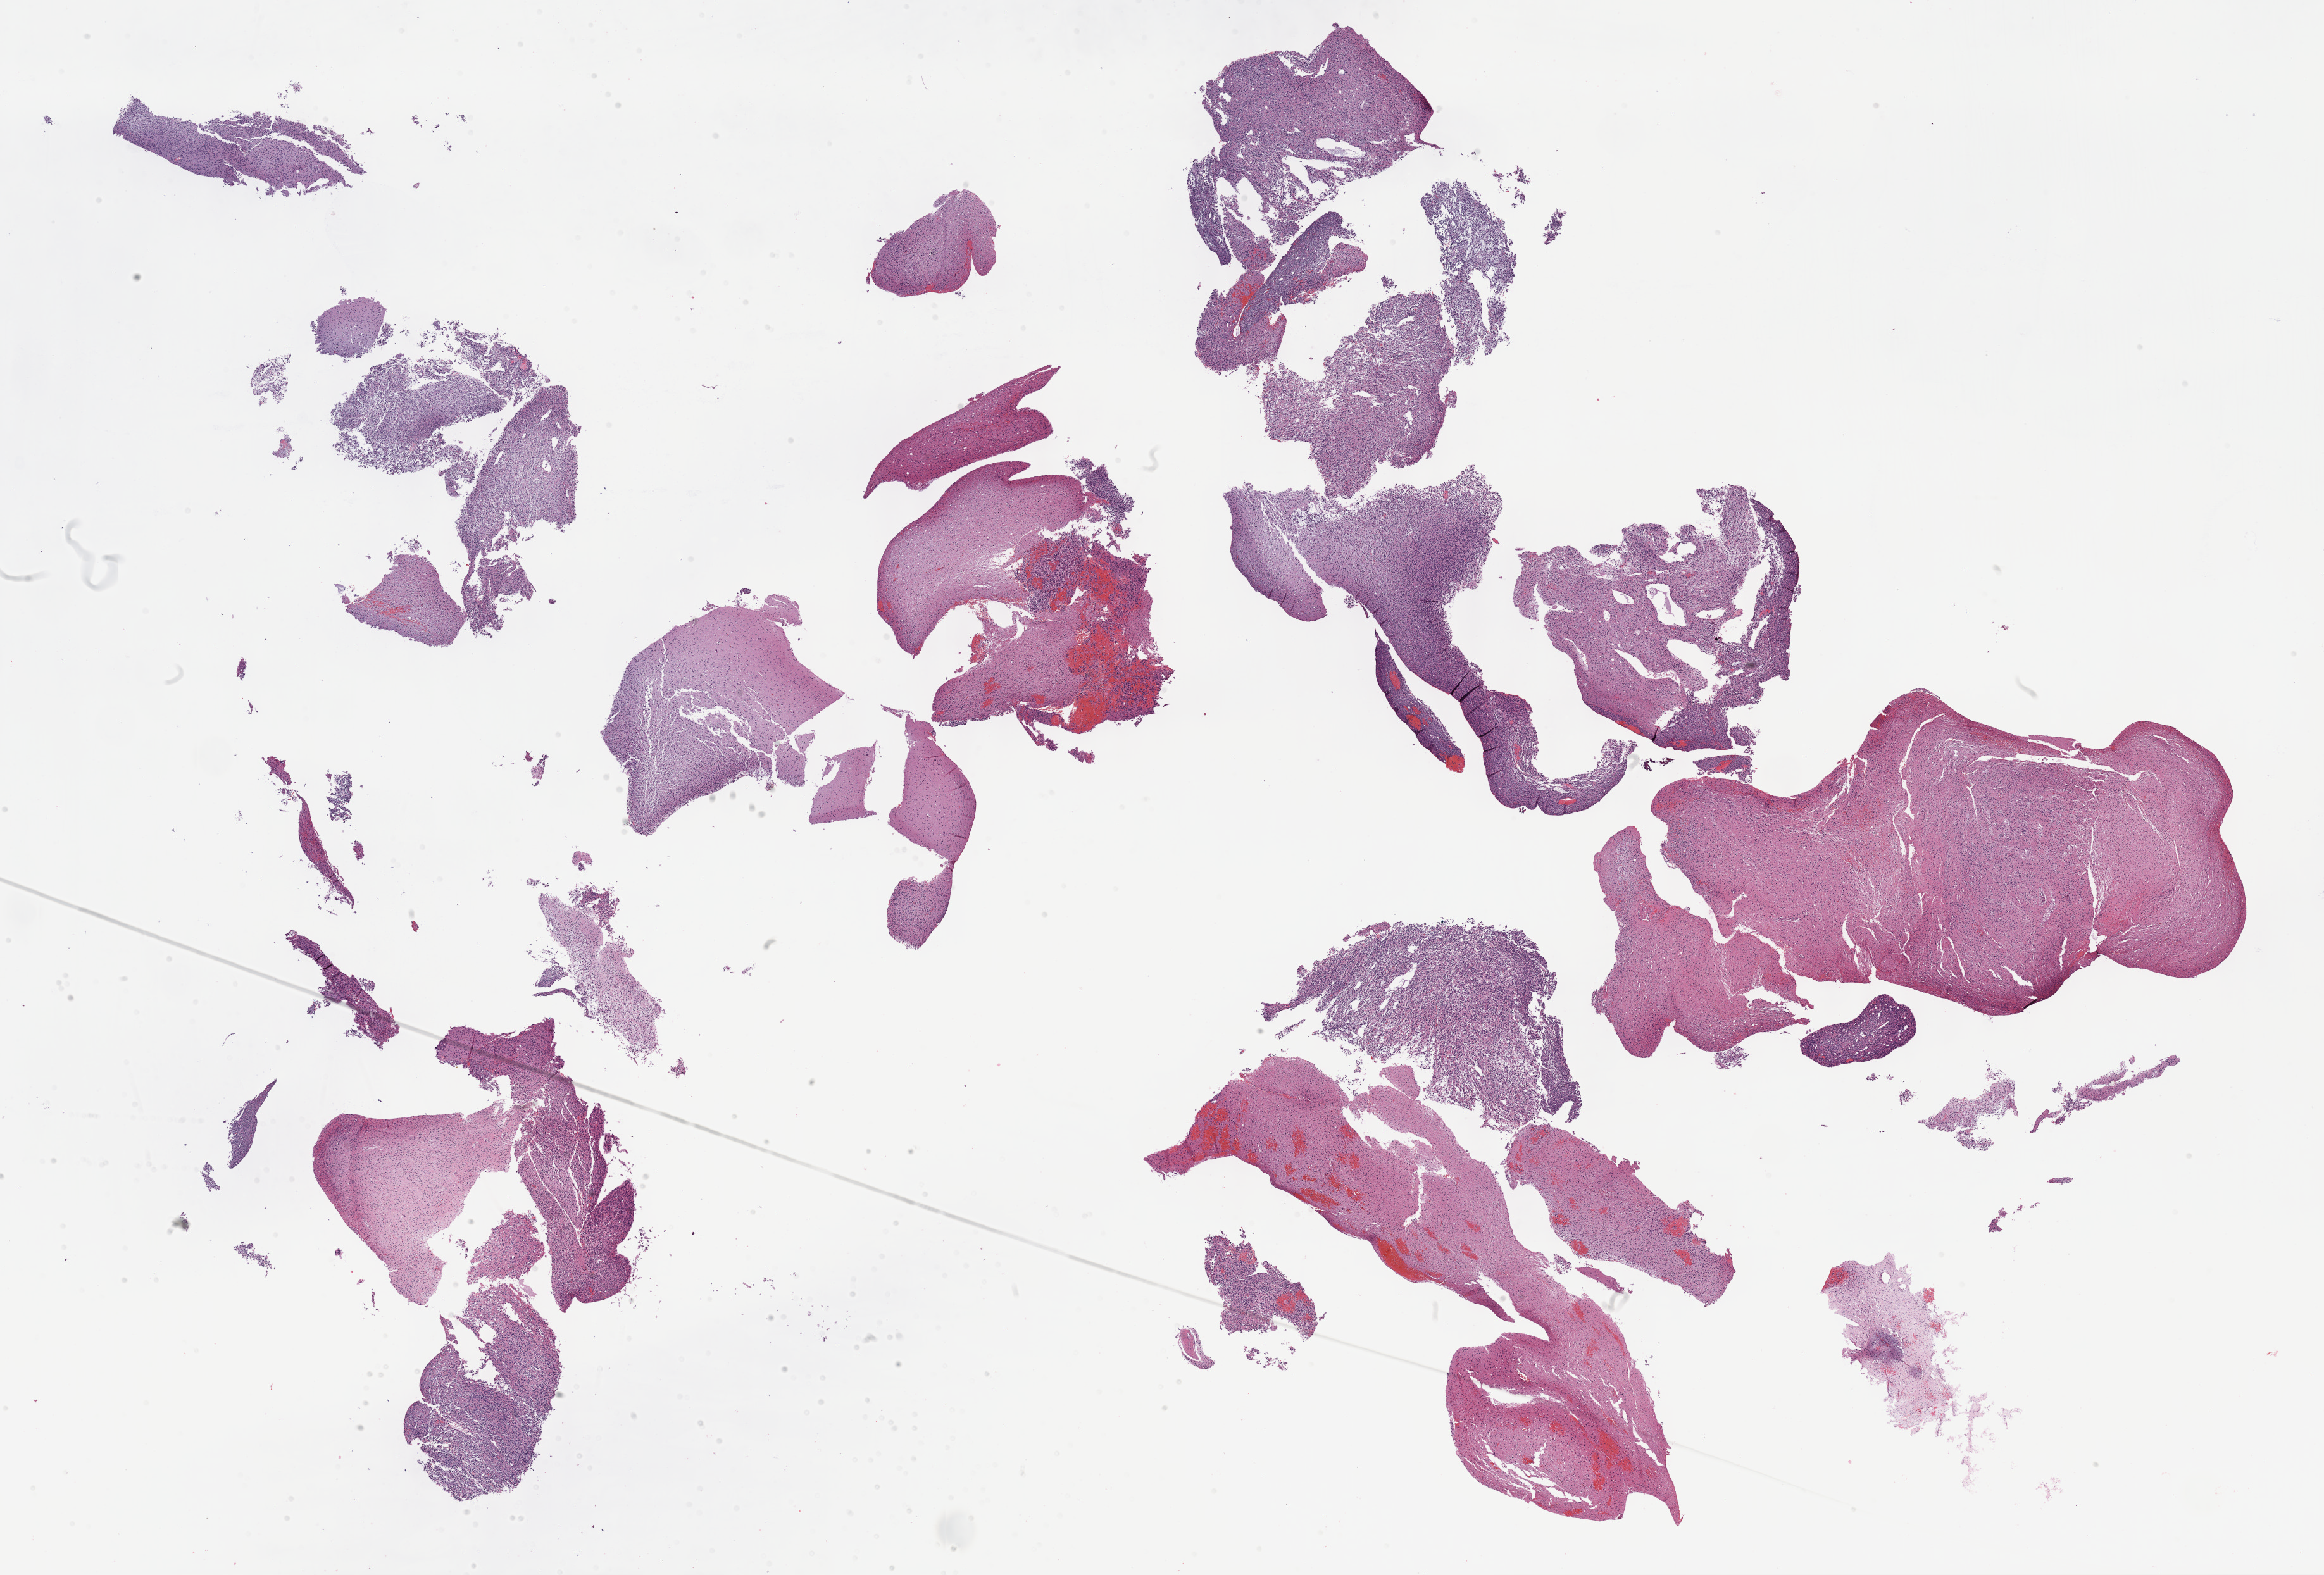
Whole-slide histology image, H&E-stained, shown as a low-resolution overview of the whole scanned area (about 29.7 x 20.1 mm, from a 40x scan); FFPE section; primary tumour sample from the brain. Patient: female, age at initial diagnosis 44 years.
Histologic diagnosis: Astrocytoma, anaplastic (cerebrum).